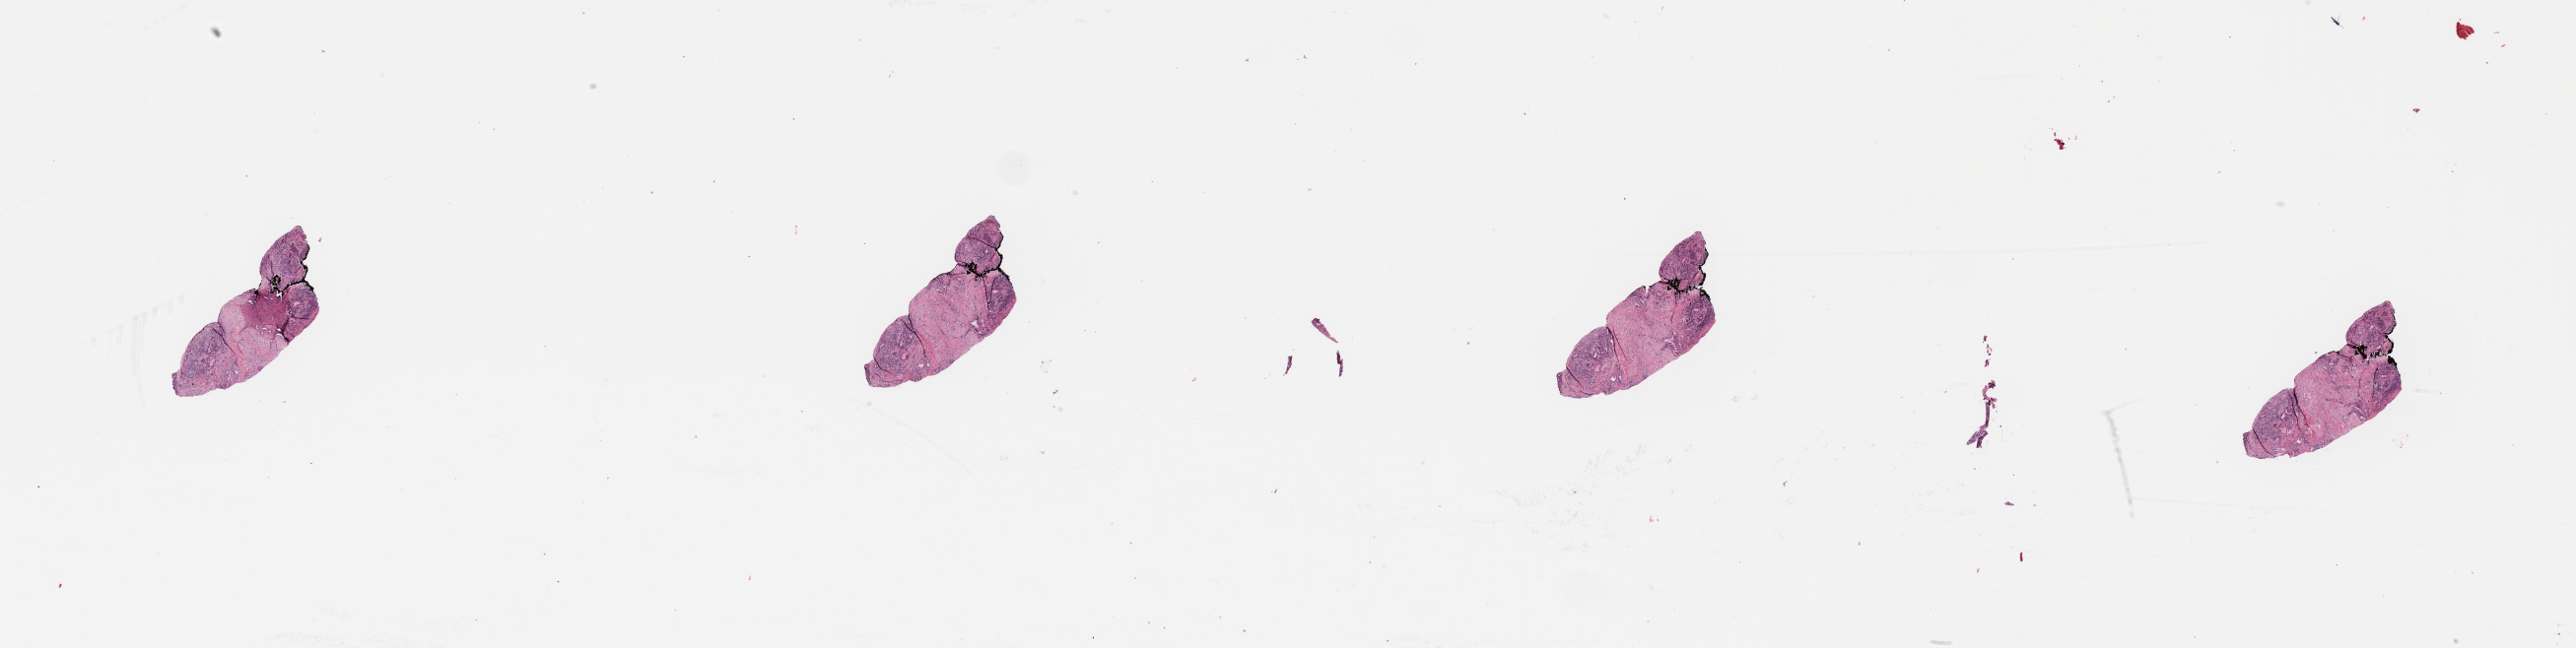
Digitized H&E tissue section (whole slide) — a low-resolution overview of the entire scanned area, about 41.3 x 10.4 mm. Tumour tissue sample, pancreas. Male, 78 y/o. Histologic grade: G2 (moderately differentiated).
Primary tumour site (as recorded): head. AJCC pathologic stage: IIB. Diagnosis: Infiltrating duct carcinoma, NOS.